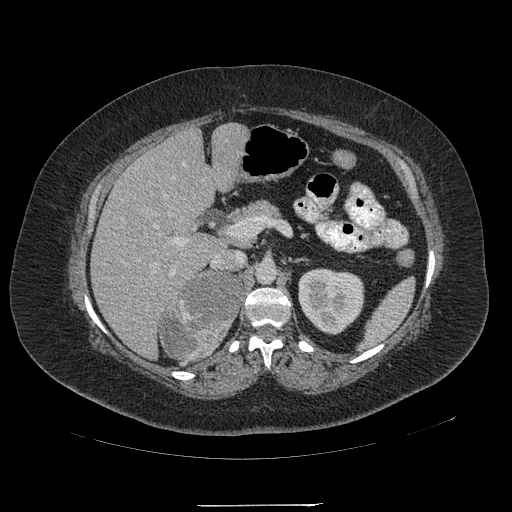
Contrast-enhanced abdominal CT, one axial slice; 120 kVp; intravenous contrast given; soft-tissue window (W 400 / L 40 HU); 1.25 mm slice thickness; 512 × 512 image matrix, field of view 453 × 453 mm. Female patient, age 55 years. Case-level facts recorded for this patient, not image findings: diagnosis: adrenocortical carcinoma; tumour side: right adrenal; tumour size at pathology: 11 cm; Ki-67 index: 20 %; stage (as recorded): 2.
Outlined on this slice (semi-automatic segmentation, software-assisted and operator-edited):
- mass: box from (x=160, y=273) to (x=241, y=359) px